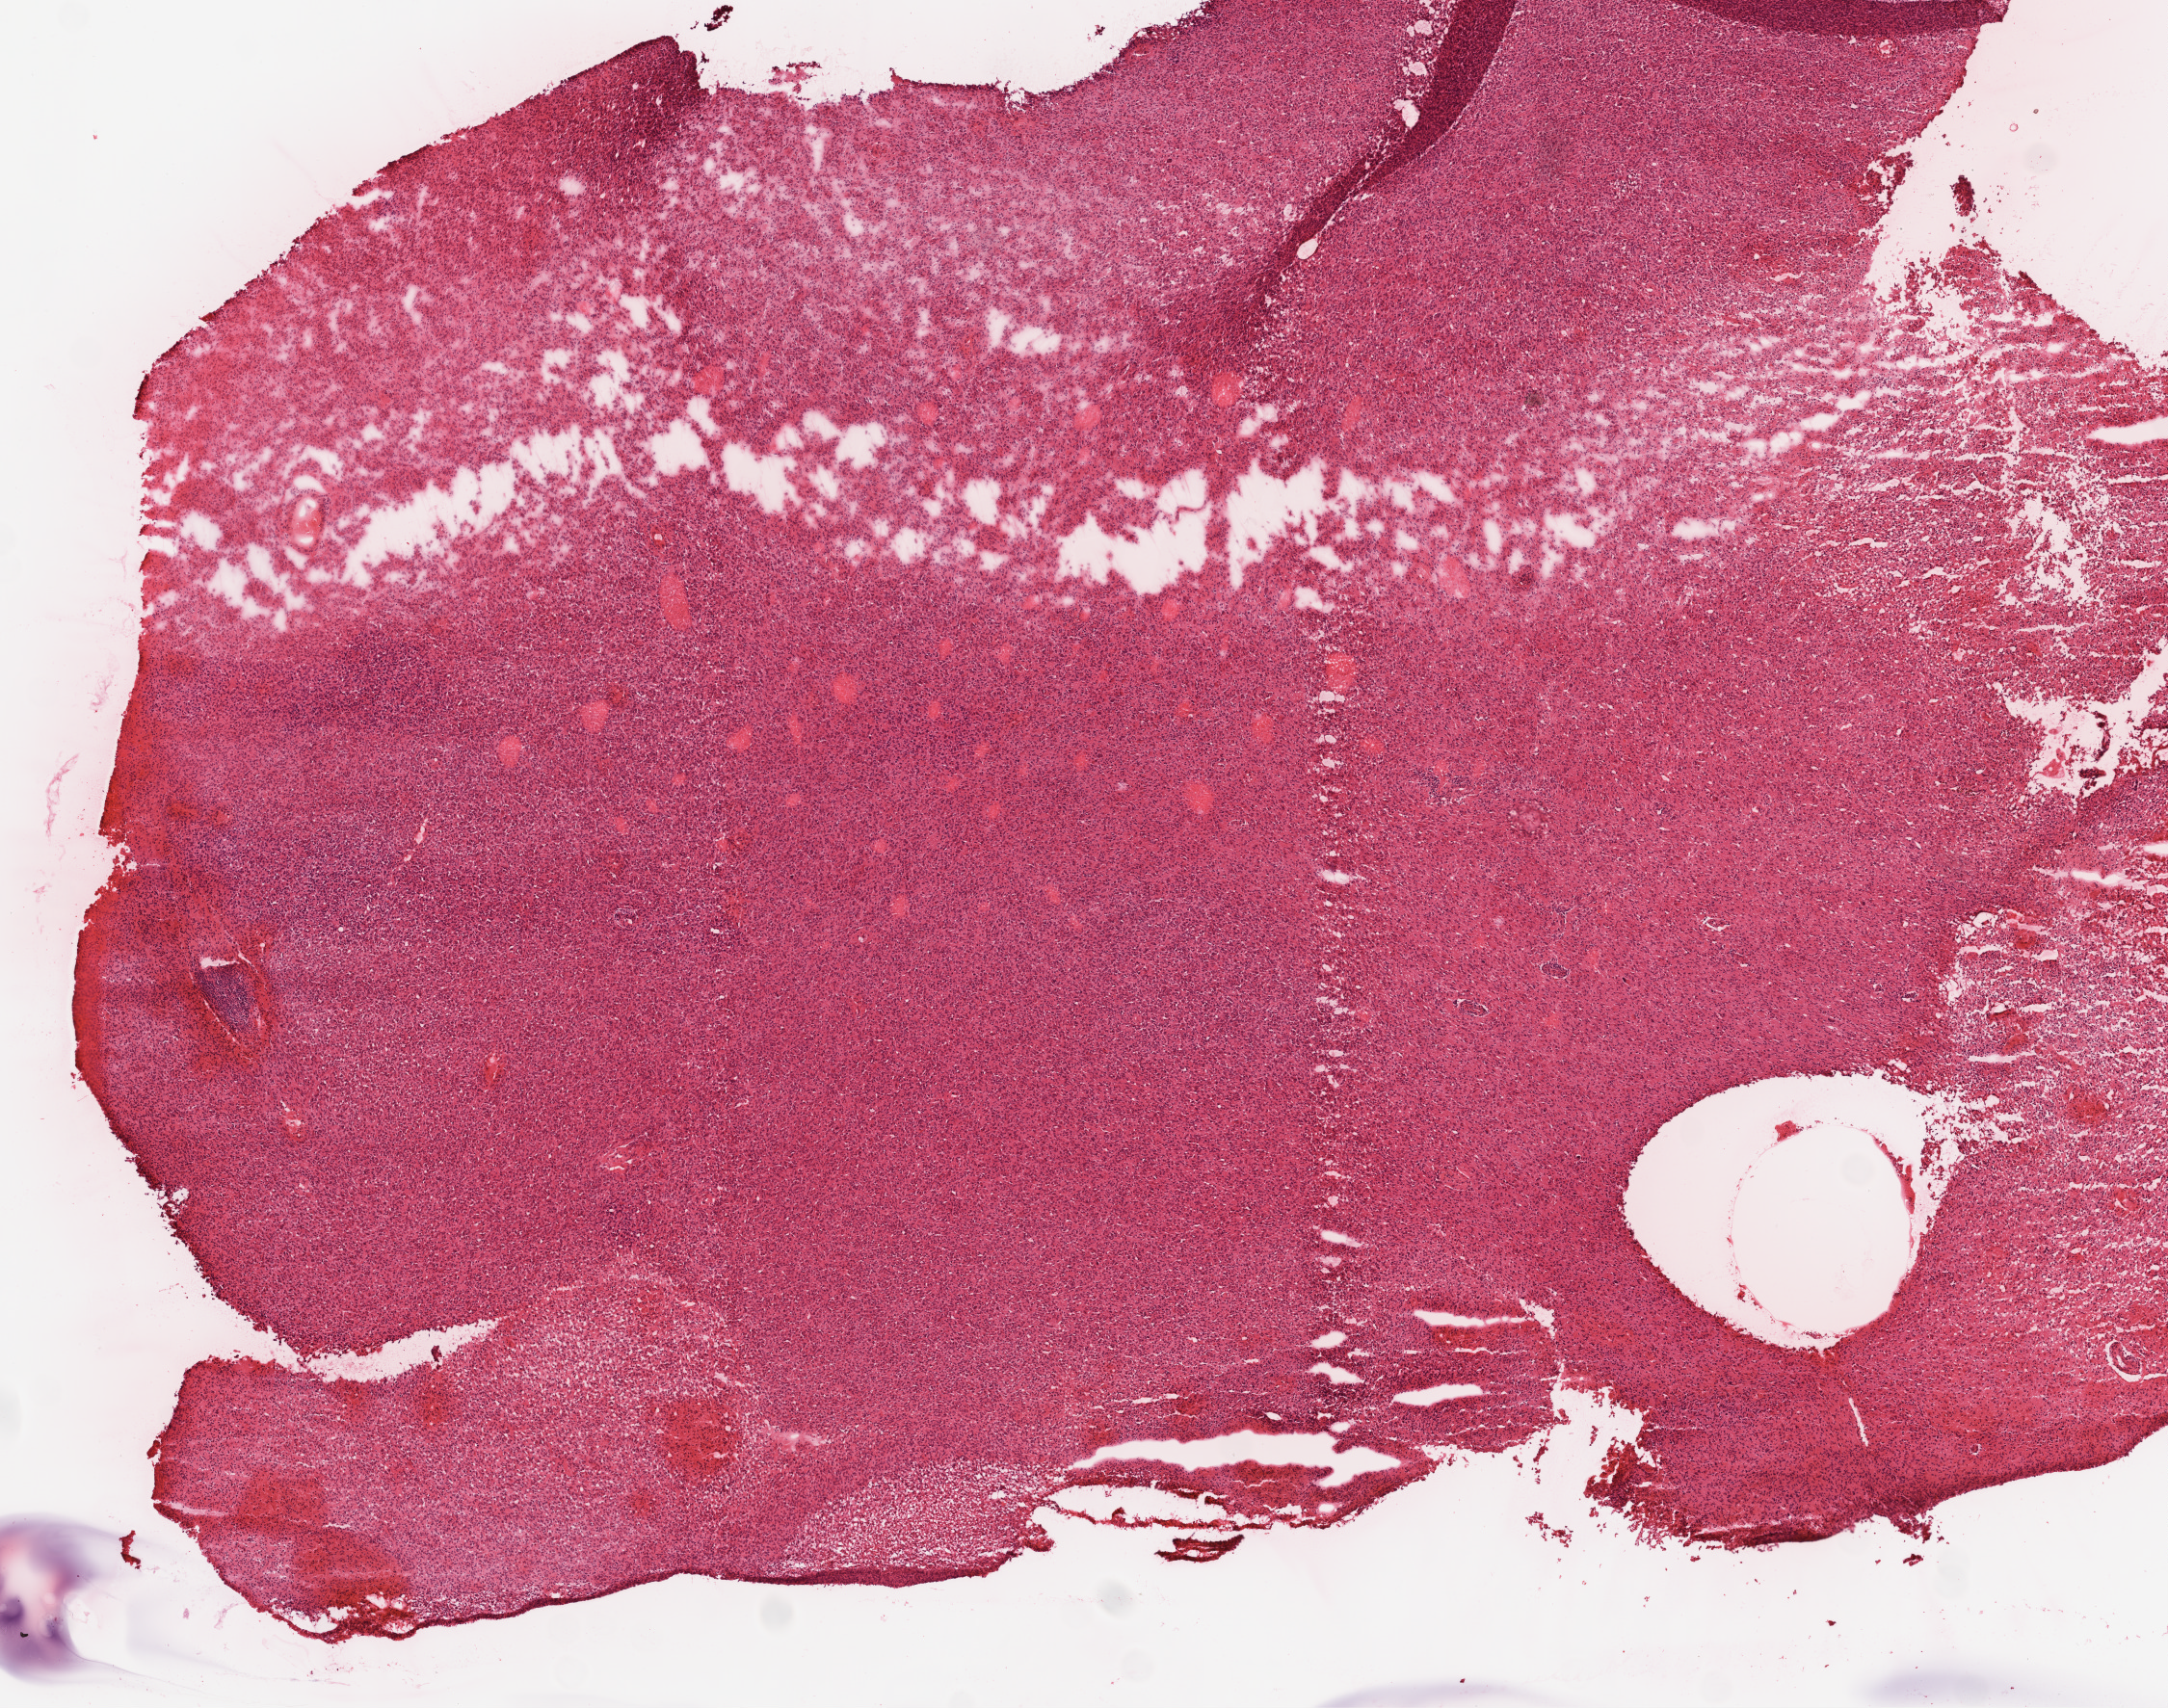
H&E whole-slide image — low-resolution overview of the scanned area, about 9.0 x 7.1 mm (slide scanned at 20x), frozen section, primary tumour sample from the brain. Female patient; age at initial diagnosis 60 years.
Histologic diagnosis: Glioblastoma.